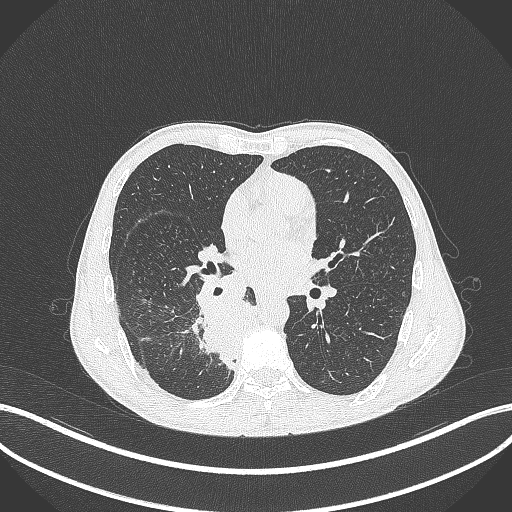
Chest CT, one axial slice. Slice 188 of 371 in the series (ordered by position). Reconstruction kernel B70f. 120 kVp. Lung window (W 1500 / L -600 HU). 512 × 512 image matrix, field of view 400 × 400 mm. Male patient, age 58 years. Case-level facts recorded for this patient, not image findings: clinical TNM (as recorded): T3 N1 M1.
Outlined on this slice (rectangle marked by the reading radiologist):
- lung tumour (recorded histology: squamous cell carcinoma): bounding box (x1, y1, x2, y2) in pixels: (190, 295, 256, 371)